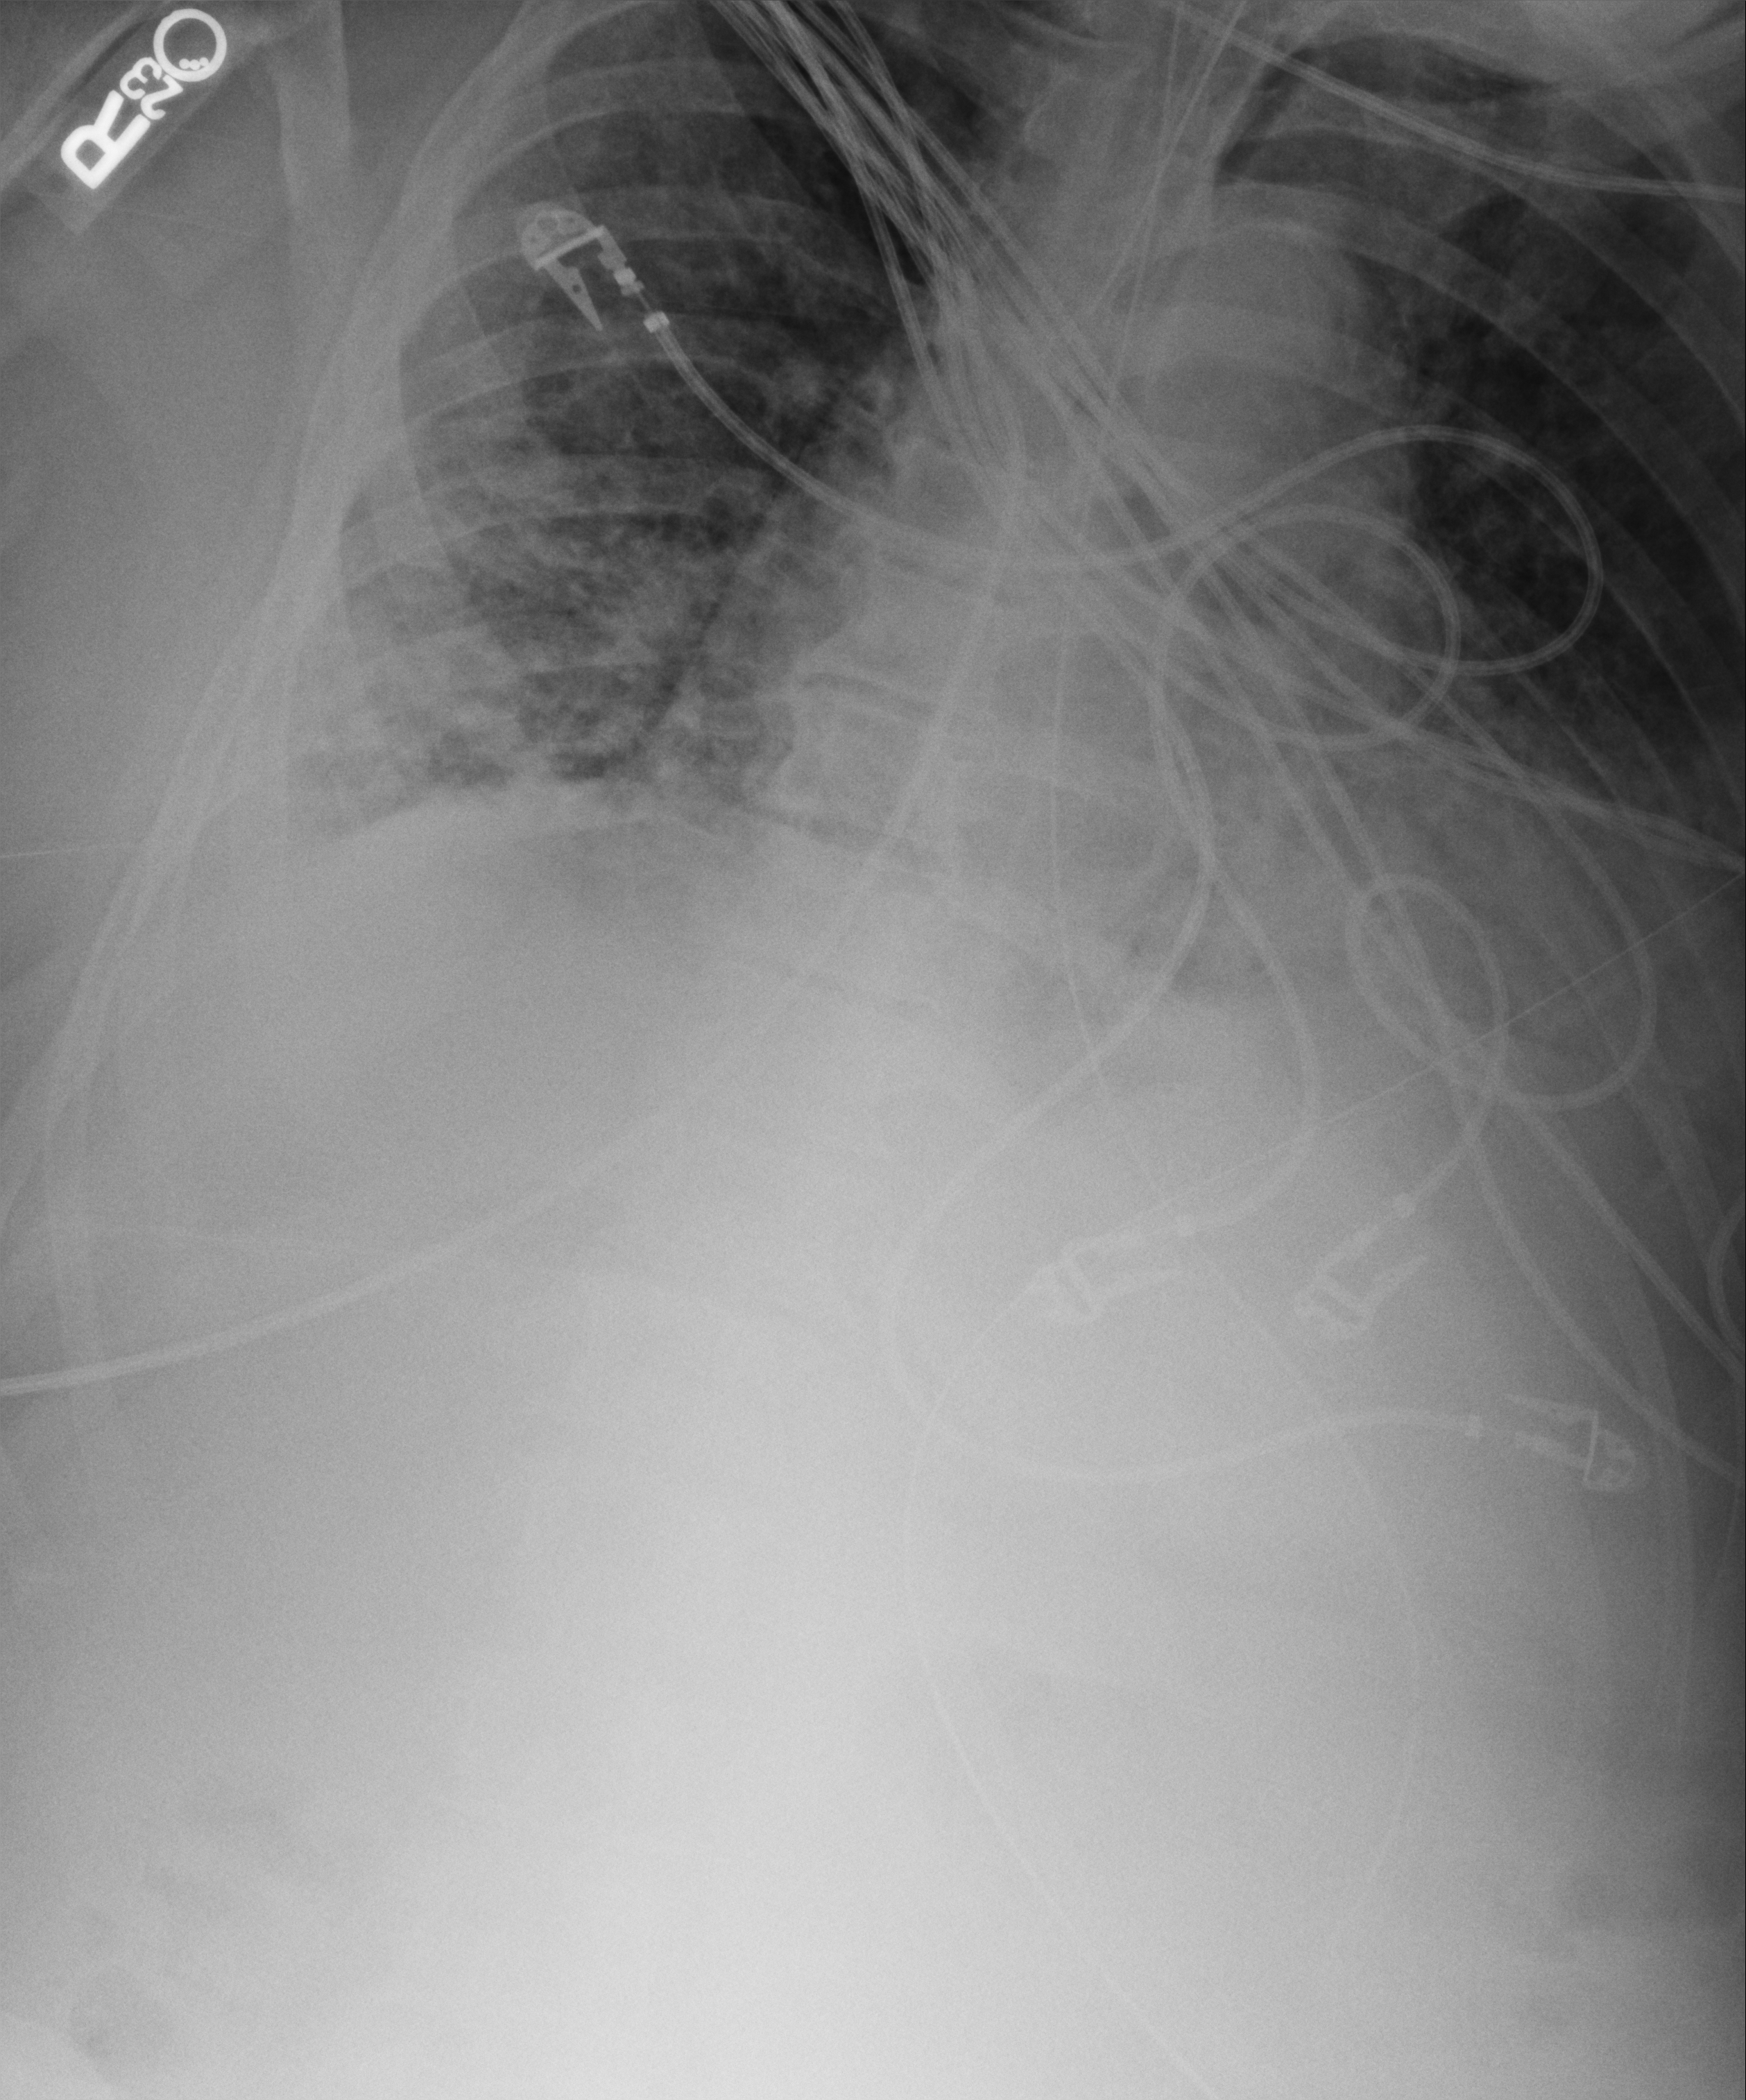
Bedside chest radiograph (computed radiography); anteroposterior (AP) projection. Male patient hospitalised with COVID-19, age 60–74 years.
Hospital-stay facts (about this admission, not read from this image; timing relative to this image not recorded):
- length of hospital stay: 40 days